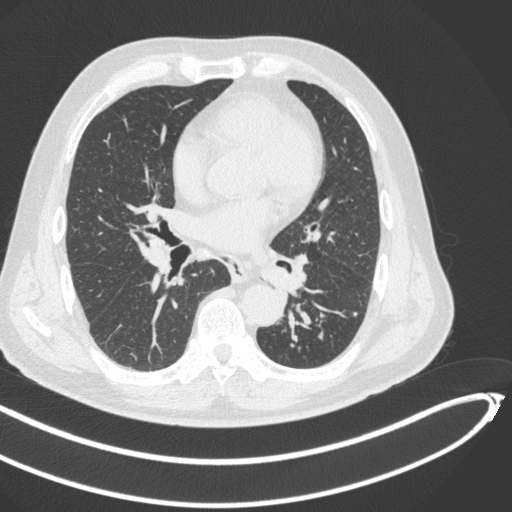
Chest CT, one axial slice; slice 236 of 466 in the series (ordered by position); reconstruction kernel B31f; 120 kVp; lung window (W 1500 / L -600 HU); 1 mm slice thickness; 512 × 512 image matrix, field of view 400 × 400 mm. Male patient, age 64 years. From the clinical record (not read from this slice): clinical TNM (as recorded): T1c N0 M0; histopathological grade: G2.
Structures marked on this image (rectangle marked by the reading radiologist):
- lung tumour (recorded histology: squamous cell carcinoma): bounding box (x1, y1, x2, y2) in pixels: (262, 260, 301, 296)